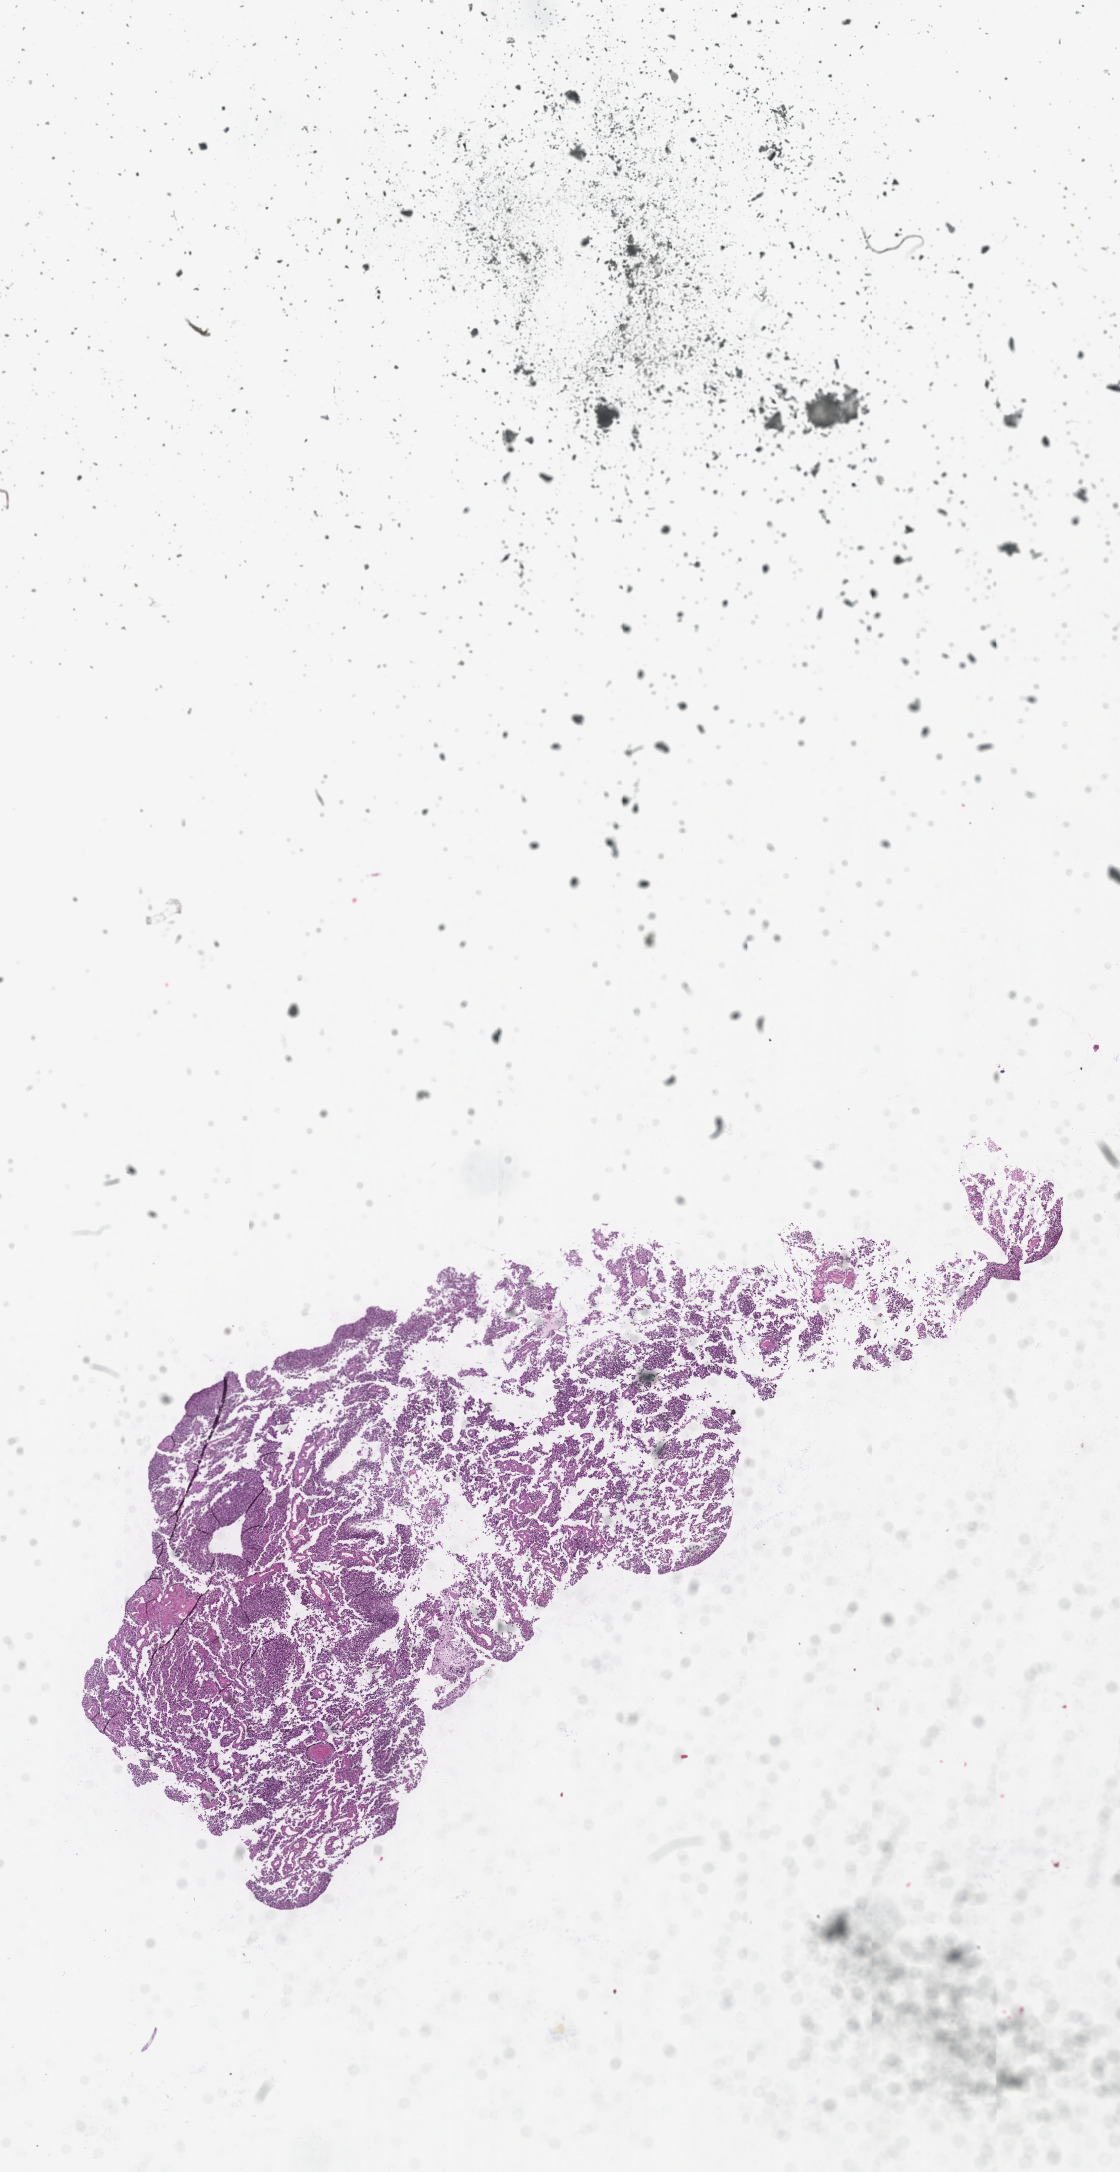
H&E whole-slide image, shown as a low-resolution overview of the whole scanned area (about 9.0 x 17.5 mm, from a 20x scan); tumour tissue sample, sampled site: brain. Female, 29 y/o. Composition of this section per pathologist review: tumour nuclei 60%, necrosis 15%.
Diagnosis: Glioblastoma.